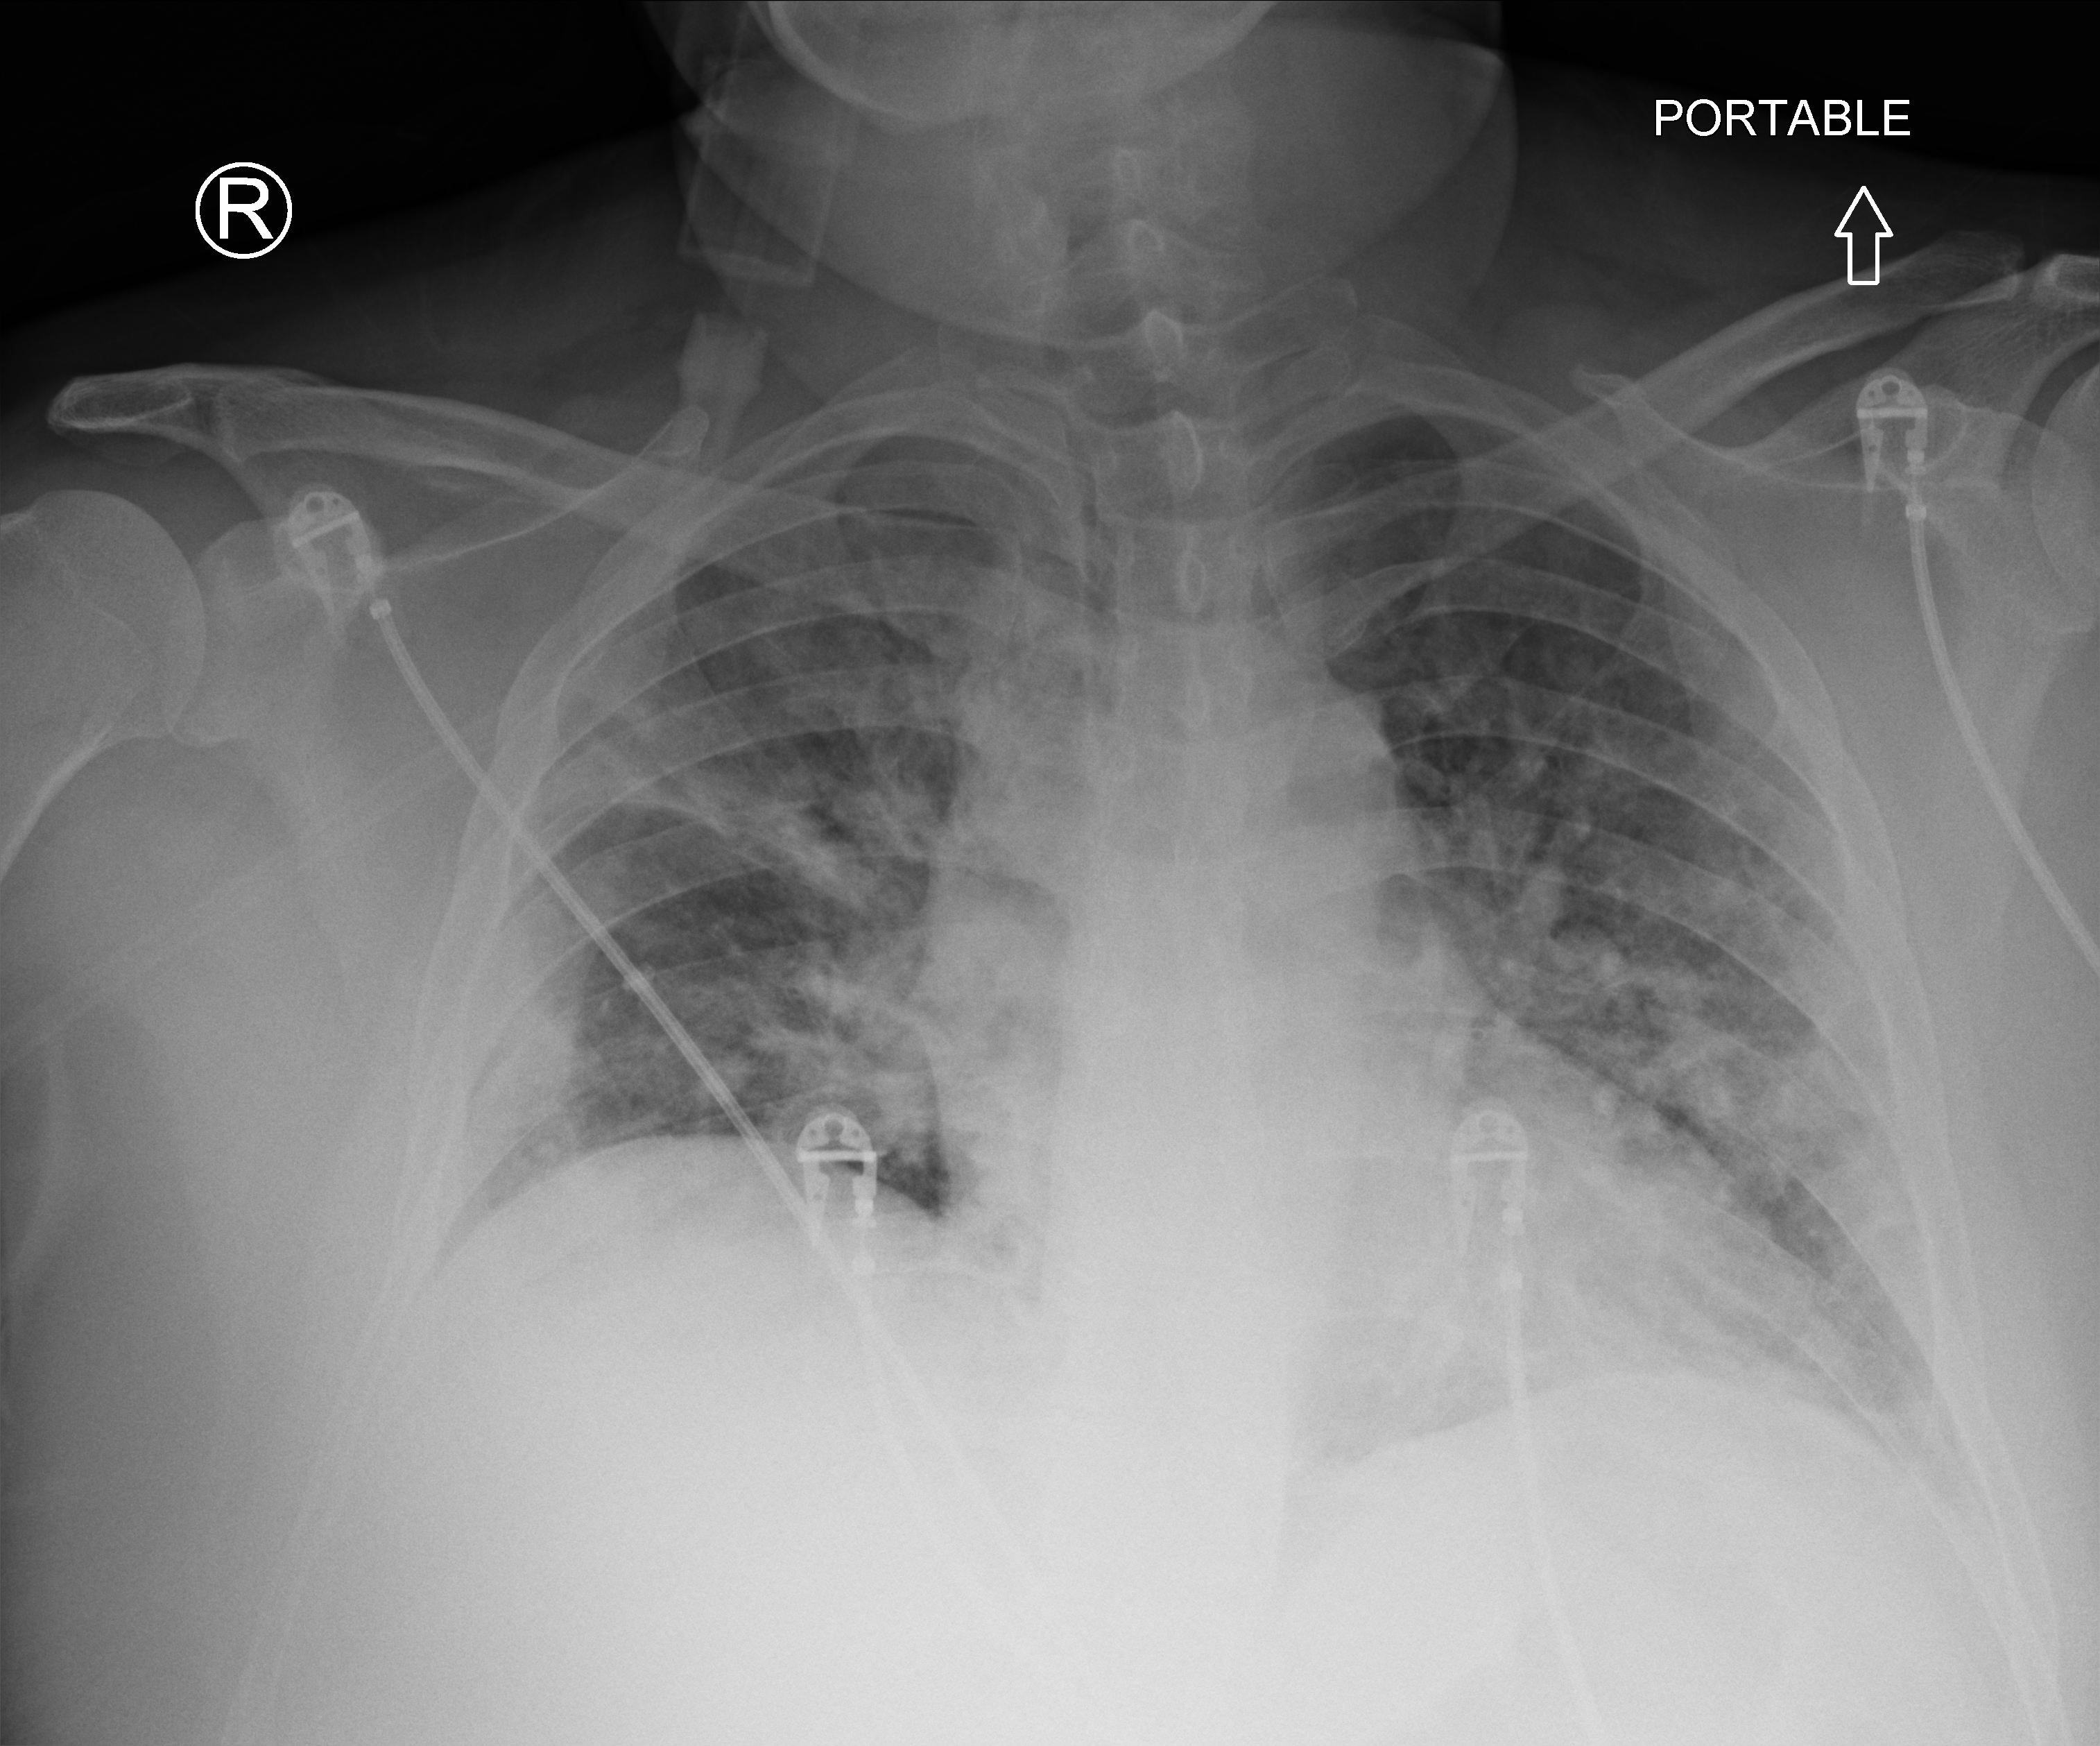
Chest X-ray (portable), anteroposterior (AP) projection. Patient hospitalised with COVID-19; male, aged 18–59 years.
Admission-level facts for this patient (not findings on this image; timing relative to this image not recorded): mechanically ventilated during this hospital stay: yes; diabetes (admission record): yes; admitted to intensive care during this hospital stay: yes.